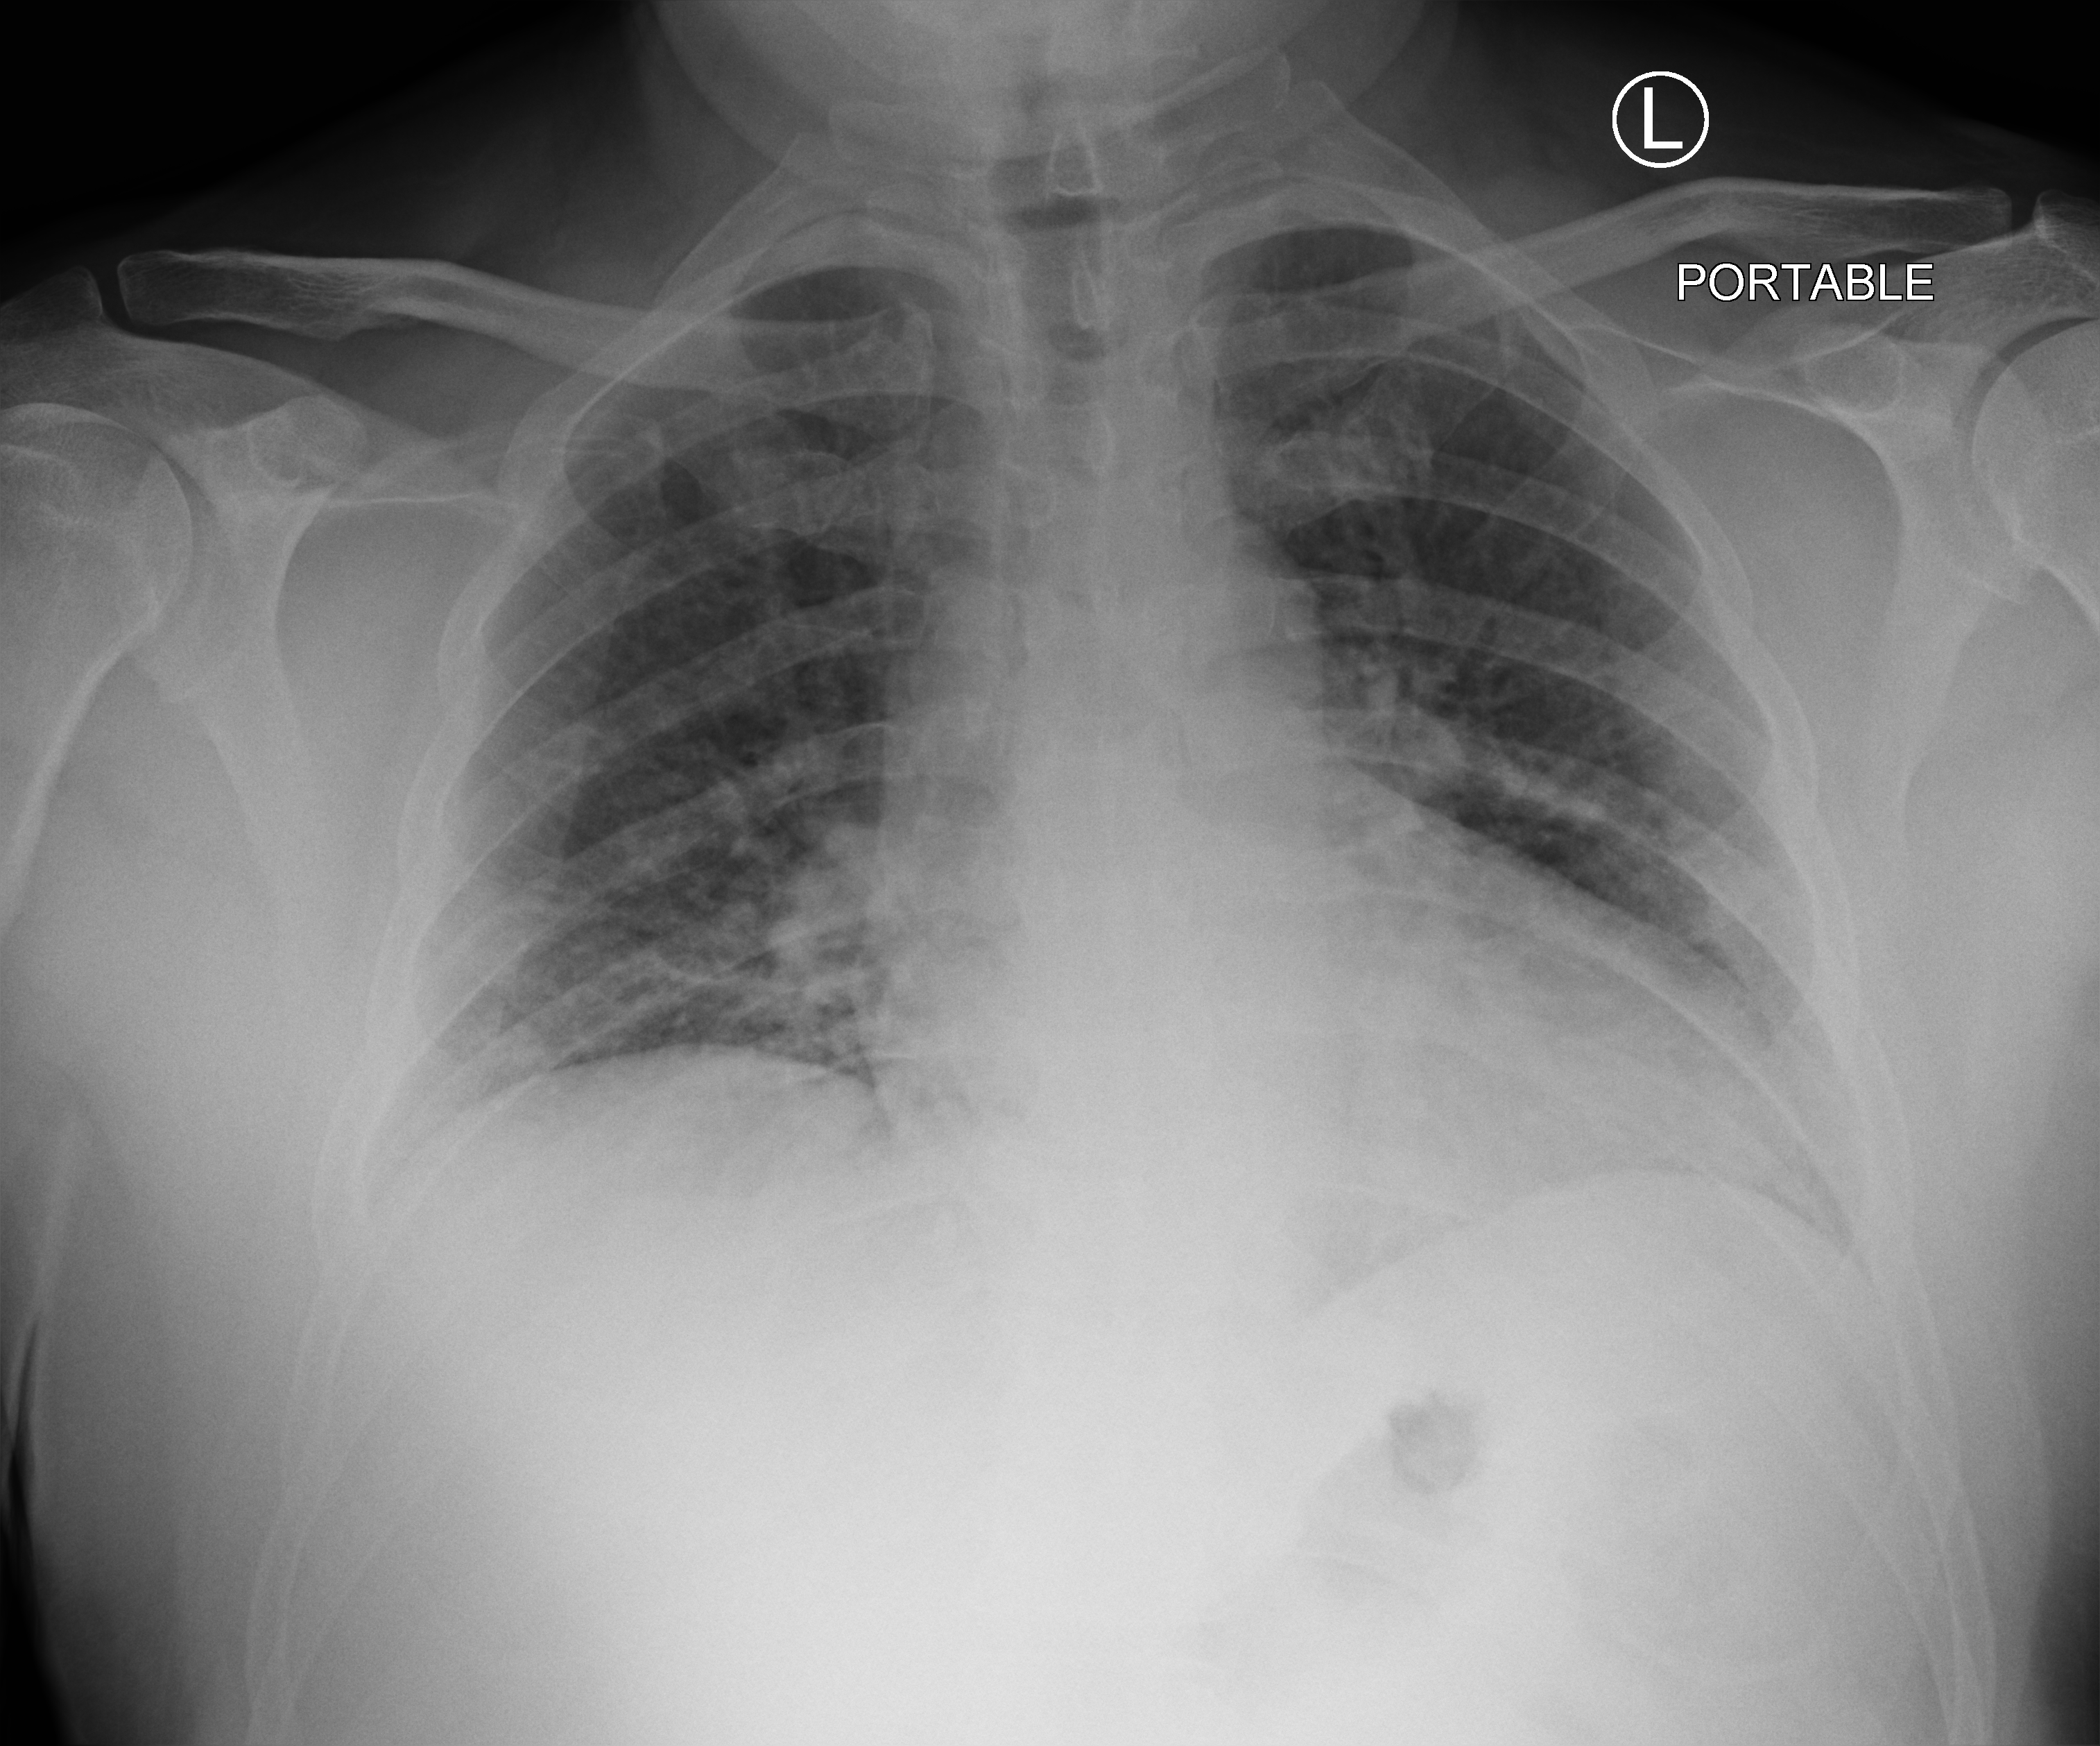
Bedside chest radiograph (computed radiography), anteroposterior (AP) projection. Male patient hospitalised with COVID-19, age 18–59 years.
Hospital-stay facts (about this admission, not read from this image; timing relative to this image not recorded): length of hospital stay: 32 days; mechanically ventilated during this hospital stay: yes; admitted to intensive care during this hospital stay: no.